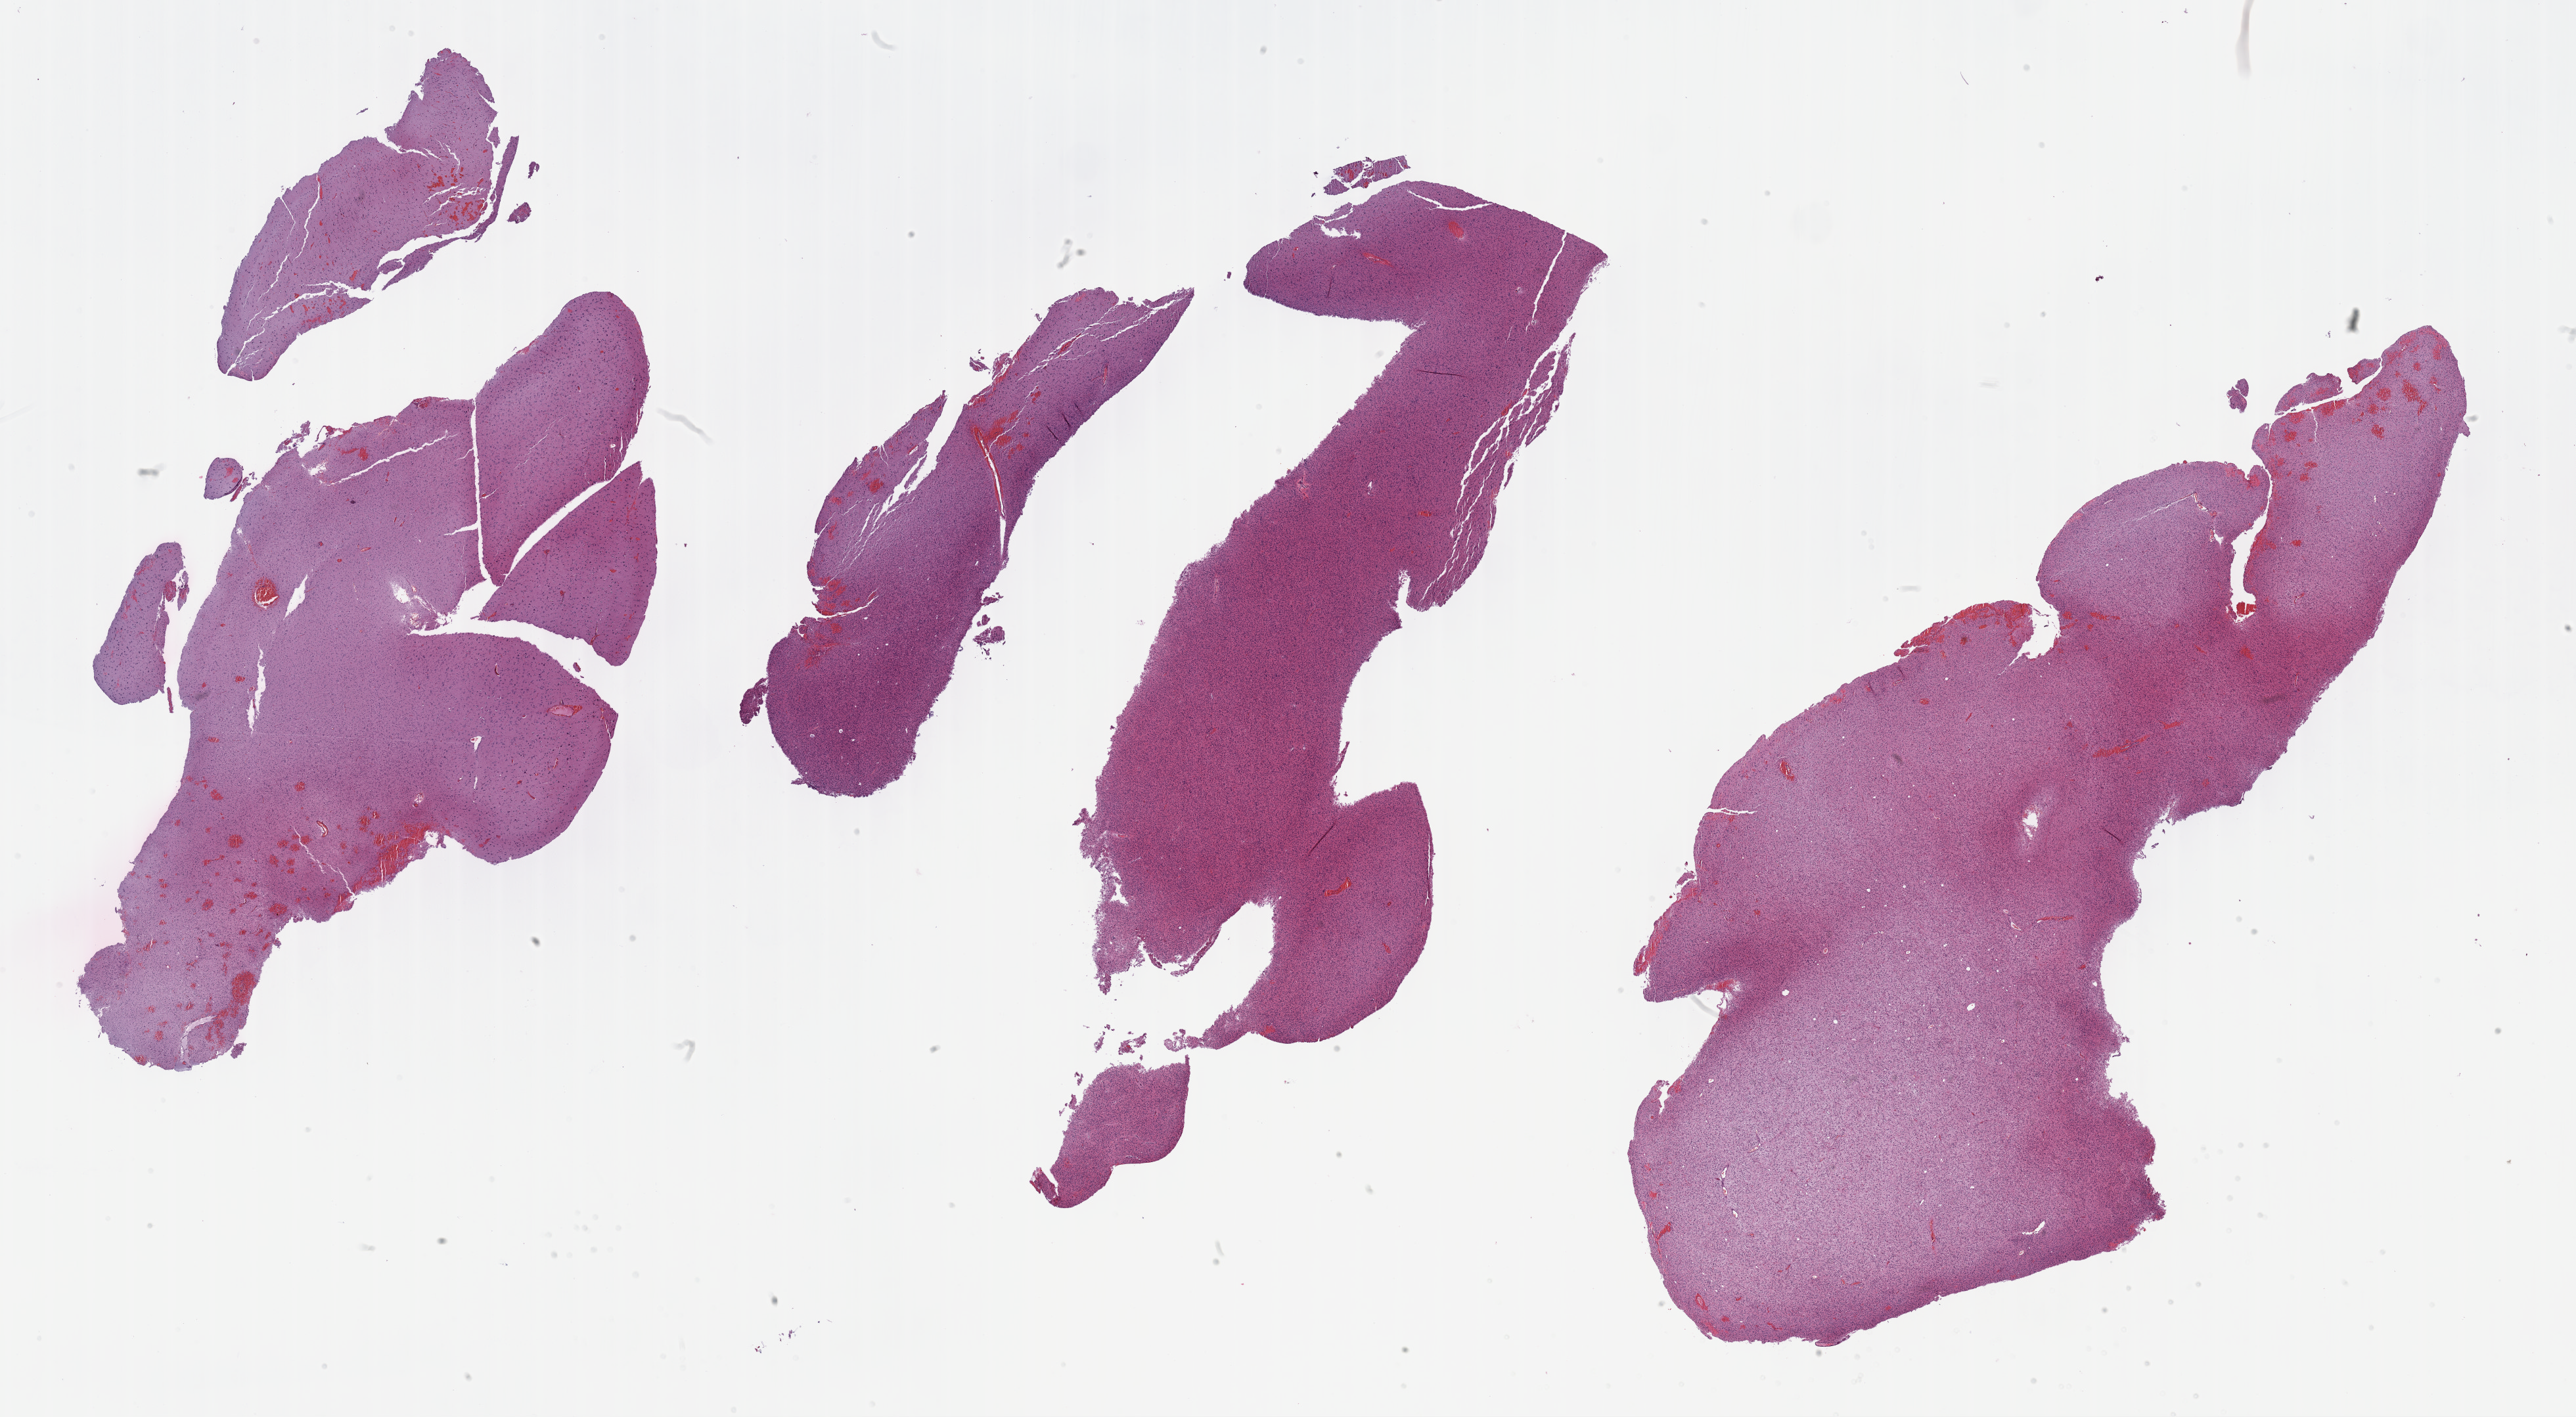
Whole-slide histology image, H&E-stained, shown as a low-resolution overview of the whole scanned area (about 31.7 x 17.4 mm), FFPE section, sample: primary tumour, brain. Male, age 25 years at initial diagnosis. Histologic grade: G2 (moderately differentiated).
Laterality: left. Diagnosis: Oligodendroglioma, NOS (cerebrum).